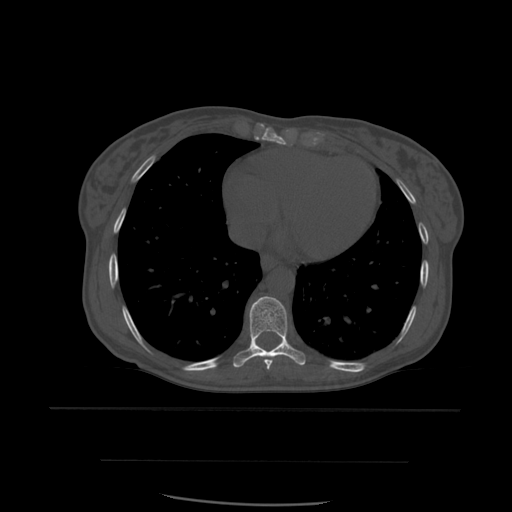
CT including the spine, one axial slice. Bone window (W 1800 / L 400 HU). 1.25 mm slice thickness. 512 × 512 image matrix, field of view 392 × 392 mm. Patient age 48 years. Case-level facts recorded for this patient, not image findings: primary cancer: lung.
Structures marked on this image (semi-automatically segmented with operator editing):
- T8 vertebra: box from (x=264, y=358) to (x=273, y=370) px
- T9 vertebra: (x=233, y=297)–(x=306, y=368)